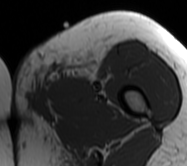
MRI of an extremity soft-tissue mass, one axial slice; position 14 of 62 along the scan axis; MR volume resampled by the dataset authors to the PET/CT grid (not the native acquisition matrix); 3.27 mm slice thickness; 187 × 166 image matrix, field of view 183 × 162 mm. Female patient. From the clinical record (not read from this slice): histological type: leiomyosarcoma; grade: high; site of the primary tumour: groin.
Structures marked on this image (expert contour drawn on MRI and transferred to this co-registered scan by the dataset authors):
- gross tumour volume including surrounding oedema: box from (x=11, y=46) to (x=97, y=121) px